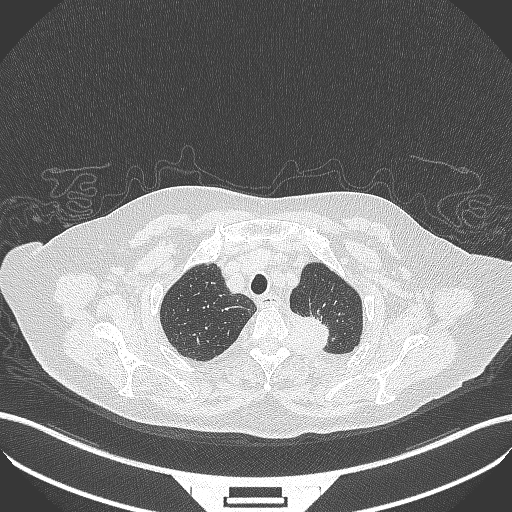
Chest CT, one axial slice. Position 297 of 353 along the scan axis. Reconstruction kernel B70f. Lung window (W 1500 / L -600 HU). 1 mm slice thickness. 512 × 512 image matrix, field of view 400 × 400 mm. Female patient, age 81 years. From the clinical record (not read from this slice): clinical TNM (as recorded): T2a N0 M0.
Structures marked on this image (rectangle marked by the reading radiologist):
- lung tumour (recorded histology: adenocarcinoma): bounding box (x1, y1, x2, y2) in pixels: (287, 306, 339, 350)